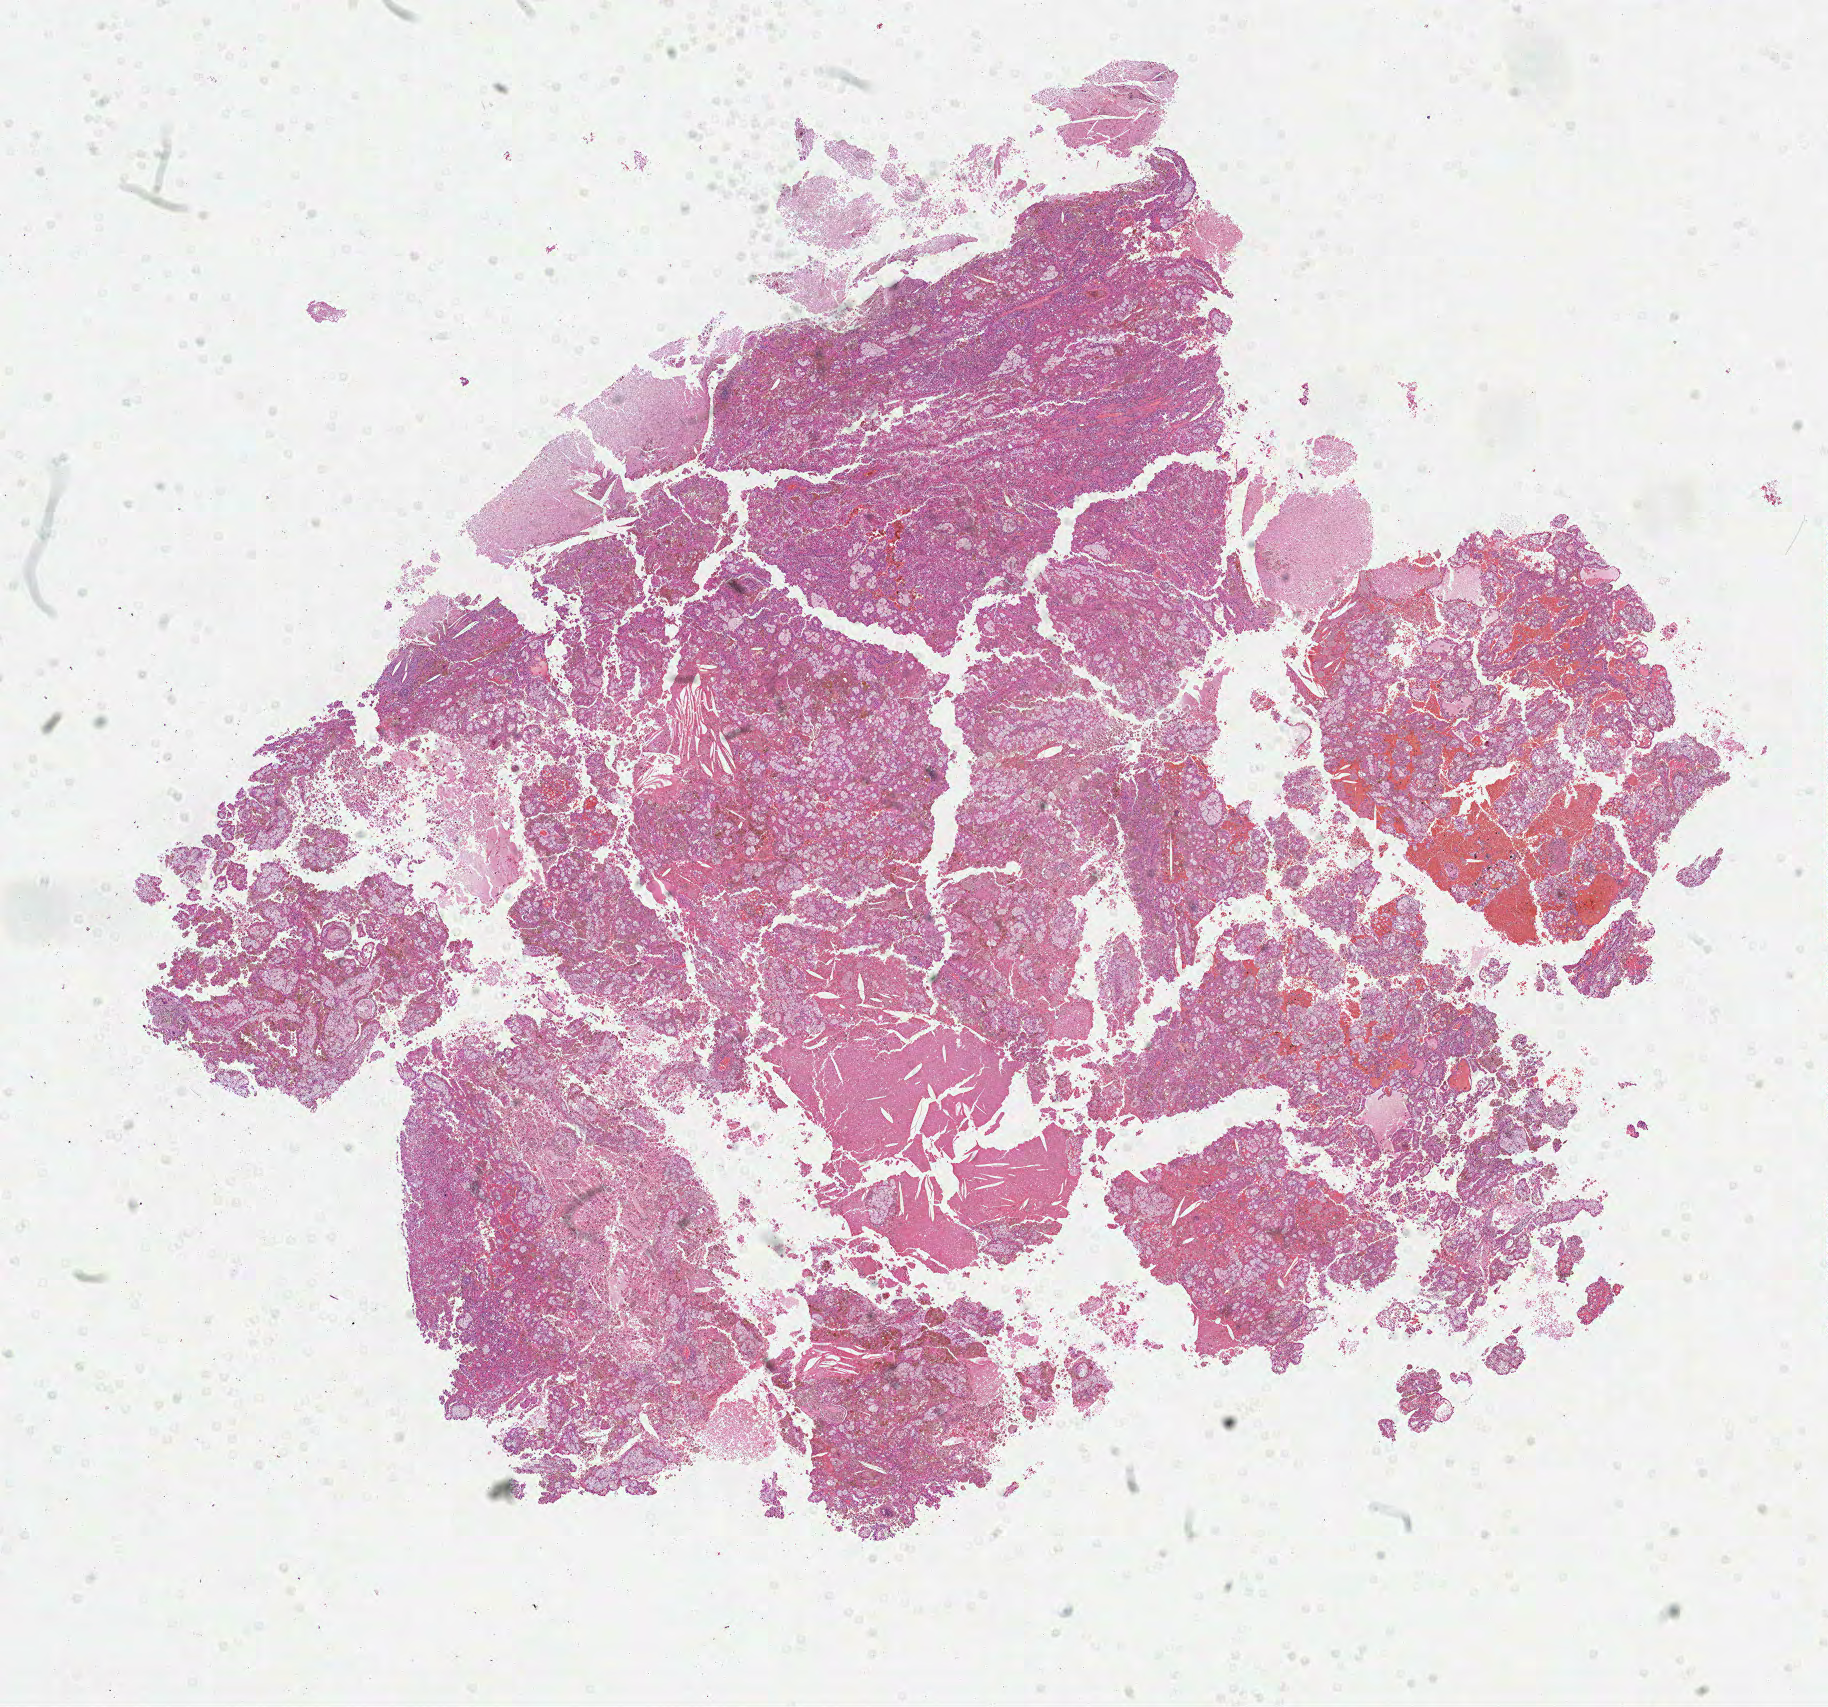
Digitized H&E-stained tissue section (whole slide) — shown as a low-resolution overview of the whole scanned area (about 14.7 x 13.8 mm, acquisition: 40x scan). Formalin-fixed paraffin-embedded (FFPE) diagnostic section. Kidney, primary tumour sample. Male patient; age at initial diagnosis 42 years.
Diagnosis: Papillary adenocarcinoma, NOS.